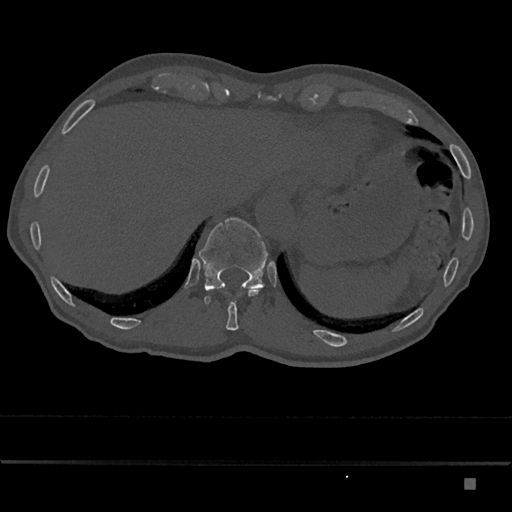
CT including the spine, one axial slice. Position 642 of 797 along the scan axis. Reconstruction kernel Br40s/3. 120 kVp. Bone window (W 1800 / L 400 HU). 0.5 mm slice thickness. 512 × 512 image matrix, field of view 390 × 390 mm. Male patient, age 72 years. From the clinical record (not read from this slice): primary cancer: prostate.
Annotated regions visible in this slice (semi-automatic segmentation, software-assisted and operator-edited):
- T11 vertebra: bounding box <212,289,259,331> (left, top, right, bottom; pixels)
- T12 vertebra: <199,217,268,305>